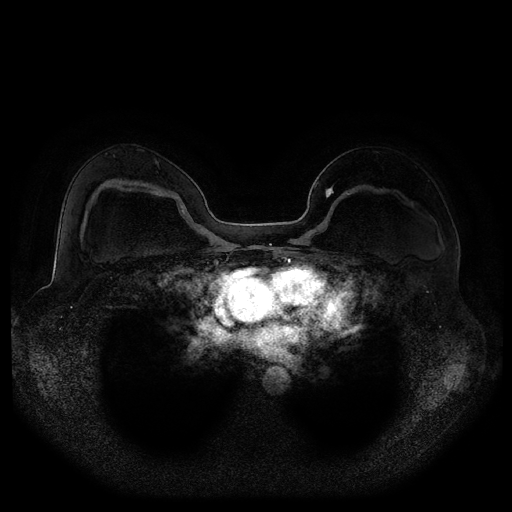
Breast MRI (dynamic contrast-enhanced, multi-phase), one axial slice. Position 66 of 116 along the scan axis. Dynamic contrast-enhanced series, time point 2 of 5 at this slice position (early post-contrast). 1.5 T. TE 2.5 ms, TR 5.2 ms. 512 × 512 image matrix, field of view 380 × 380 mm. Female patient, age 43 years.
Structures marked on this image (semi-automatically segmented with operator editing):
- breast lesion (labelled benign in the annotation): bounding box (x1, y1, x2, y2) in pixels: (325, 185, 334, 199)